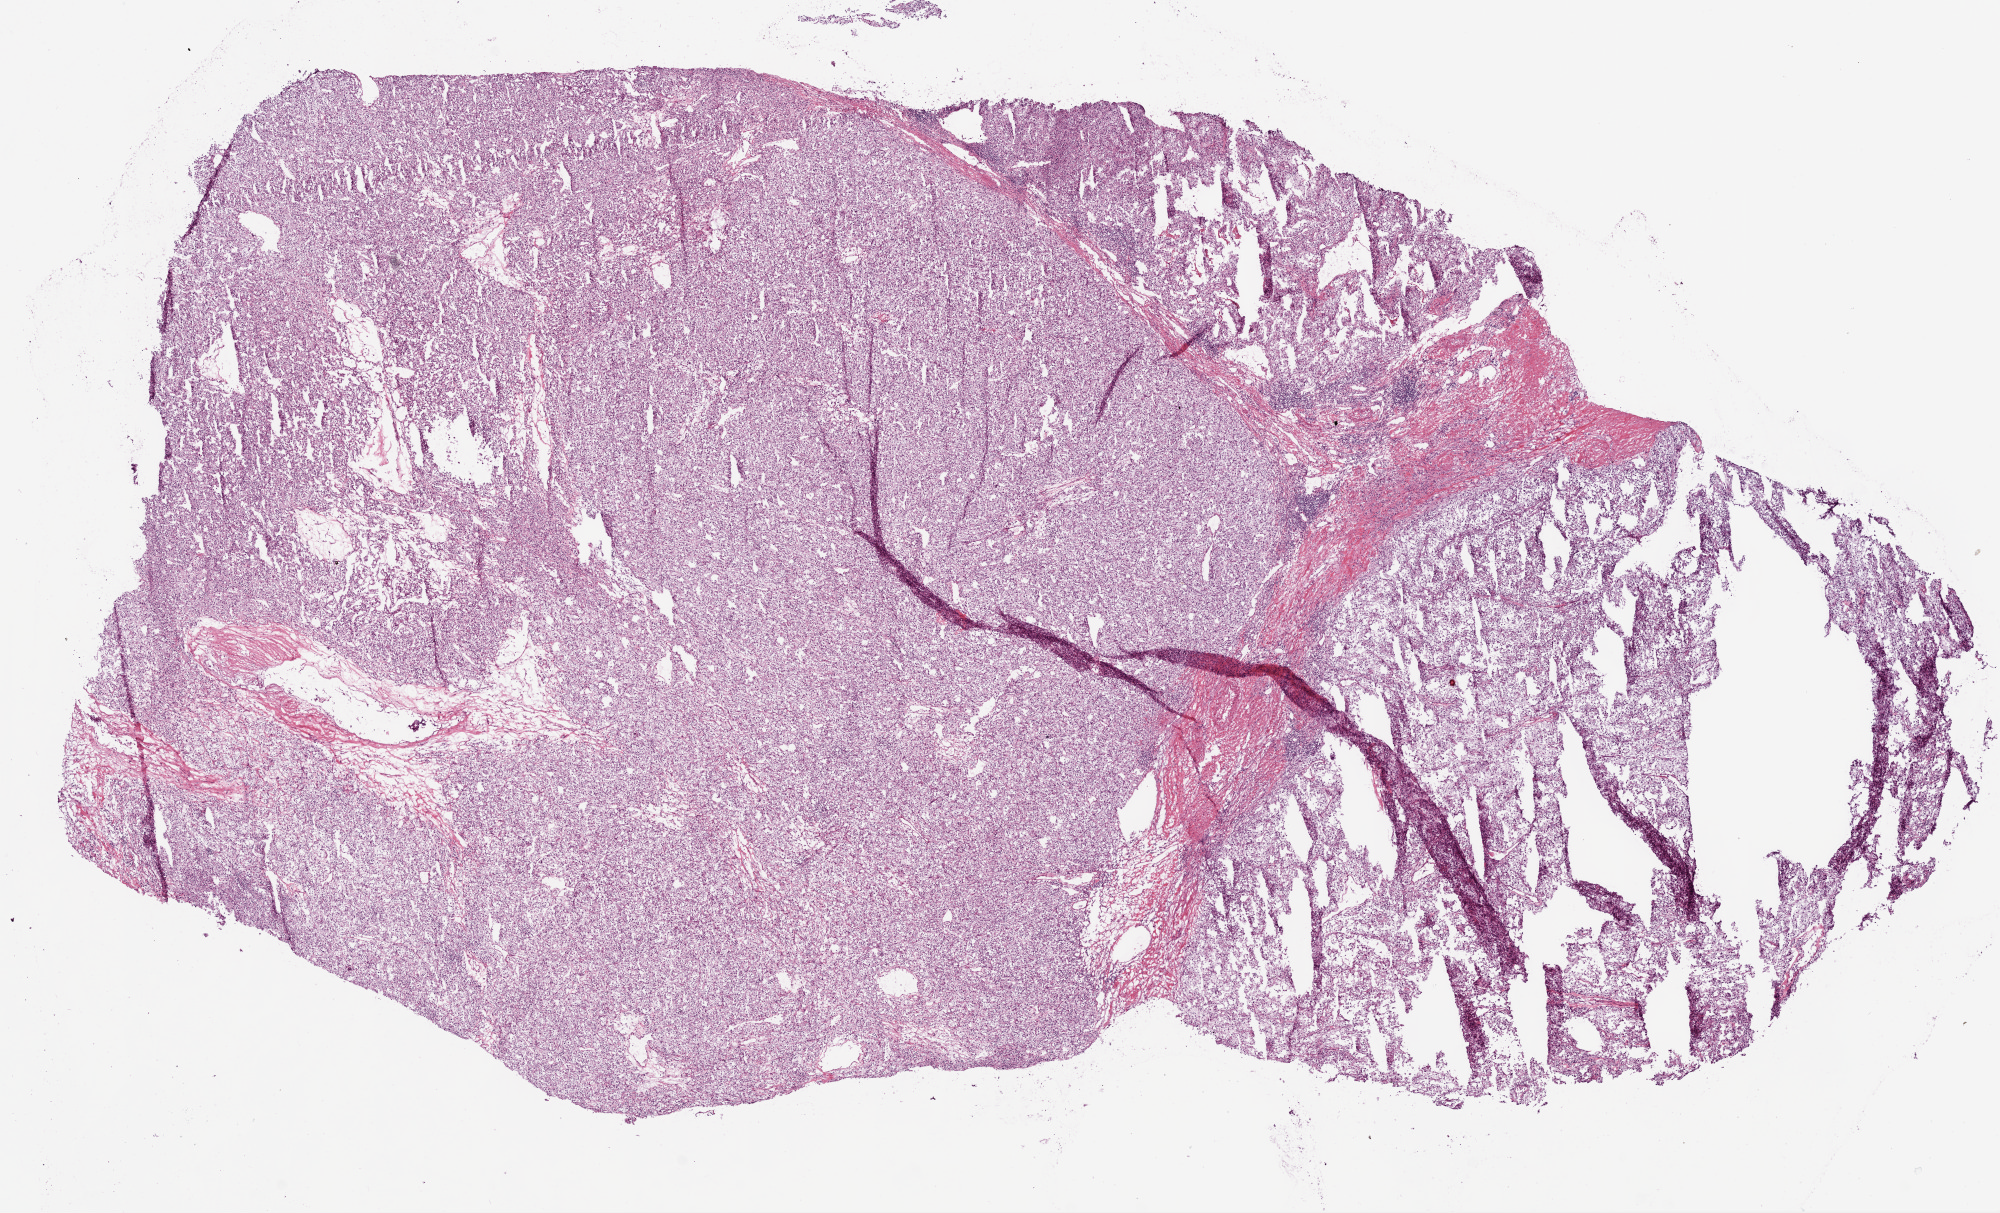
Digitized H&E-stained tissue section (whole slide) — low-resolution overview of the scanned area, about 16.0 x 9.7 mm (slide scanned at 20x), frozen section from the bottom of the tissue portion, kidney, primary tumour sample. Patient: male, age at initial diagnosis 54 years. Histologic grade: G3 (poorly differentiated). Slide review estimates, as recorded: tumour cells 90%, tumour nuclei 85%, normal cells 0%, stromal cells 10%, necrosis 0%.
* diagnosis: Clear cell adenocarcinoma, NOS
* TNM: T3b NX M0
* AJCC pathologic stage: III
* laterality: left